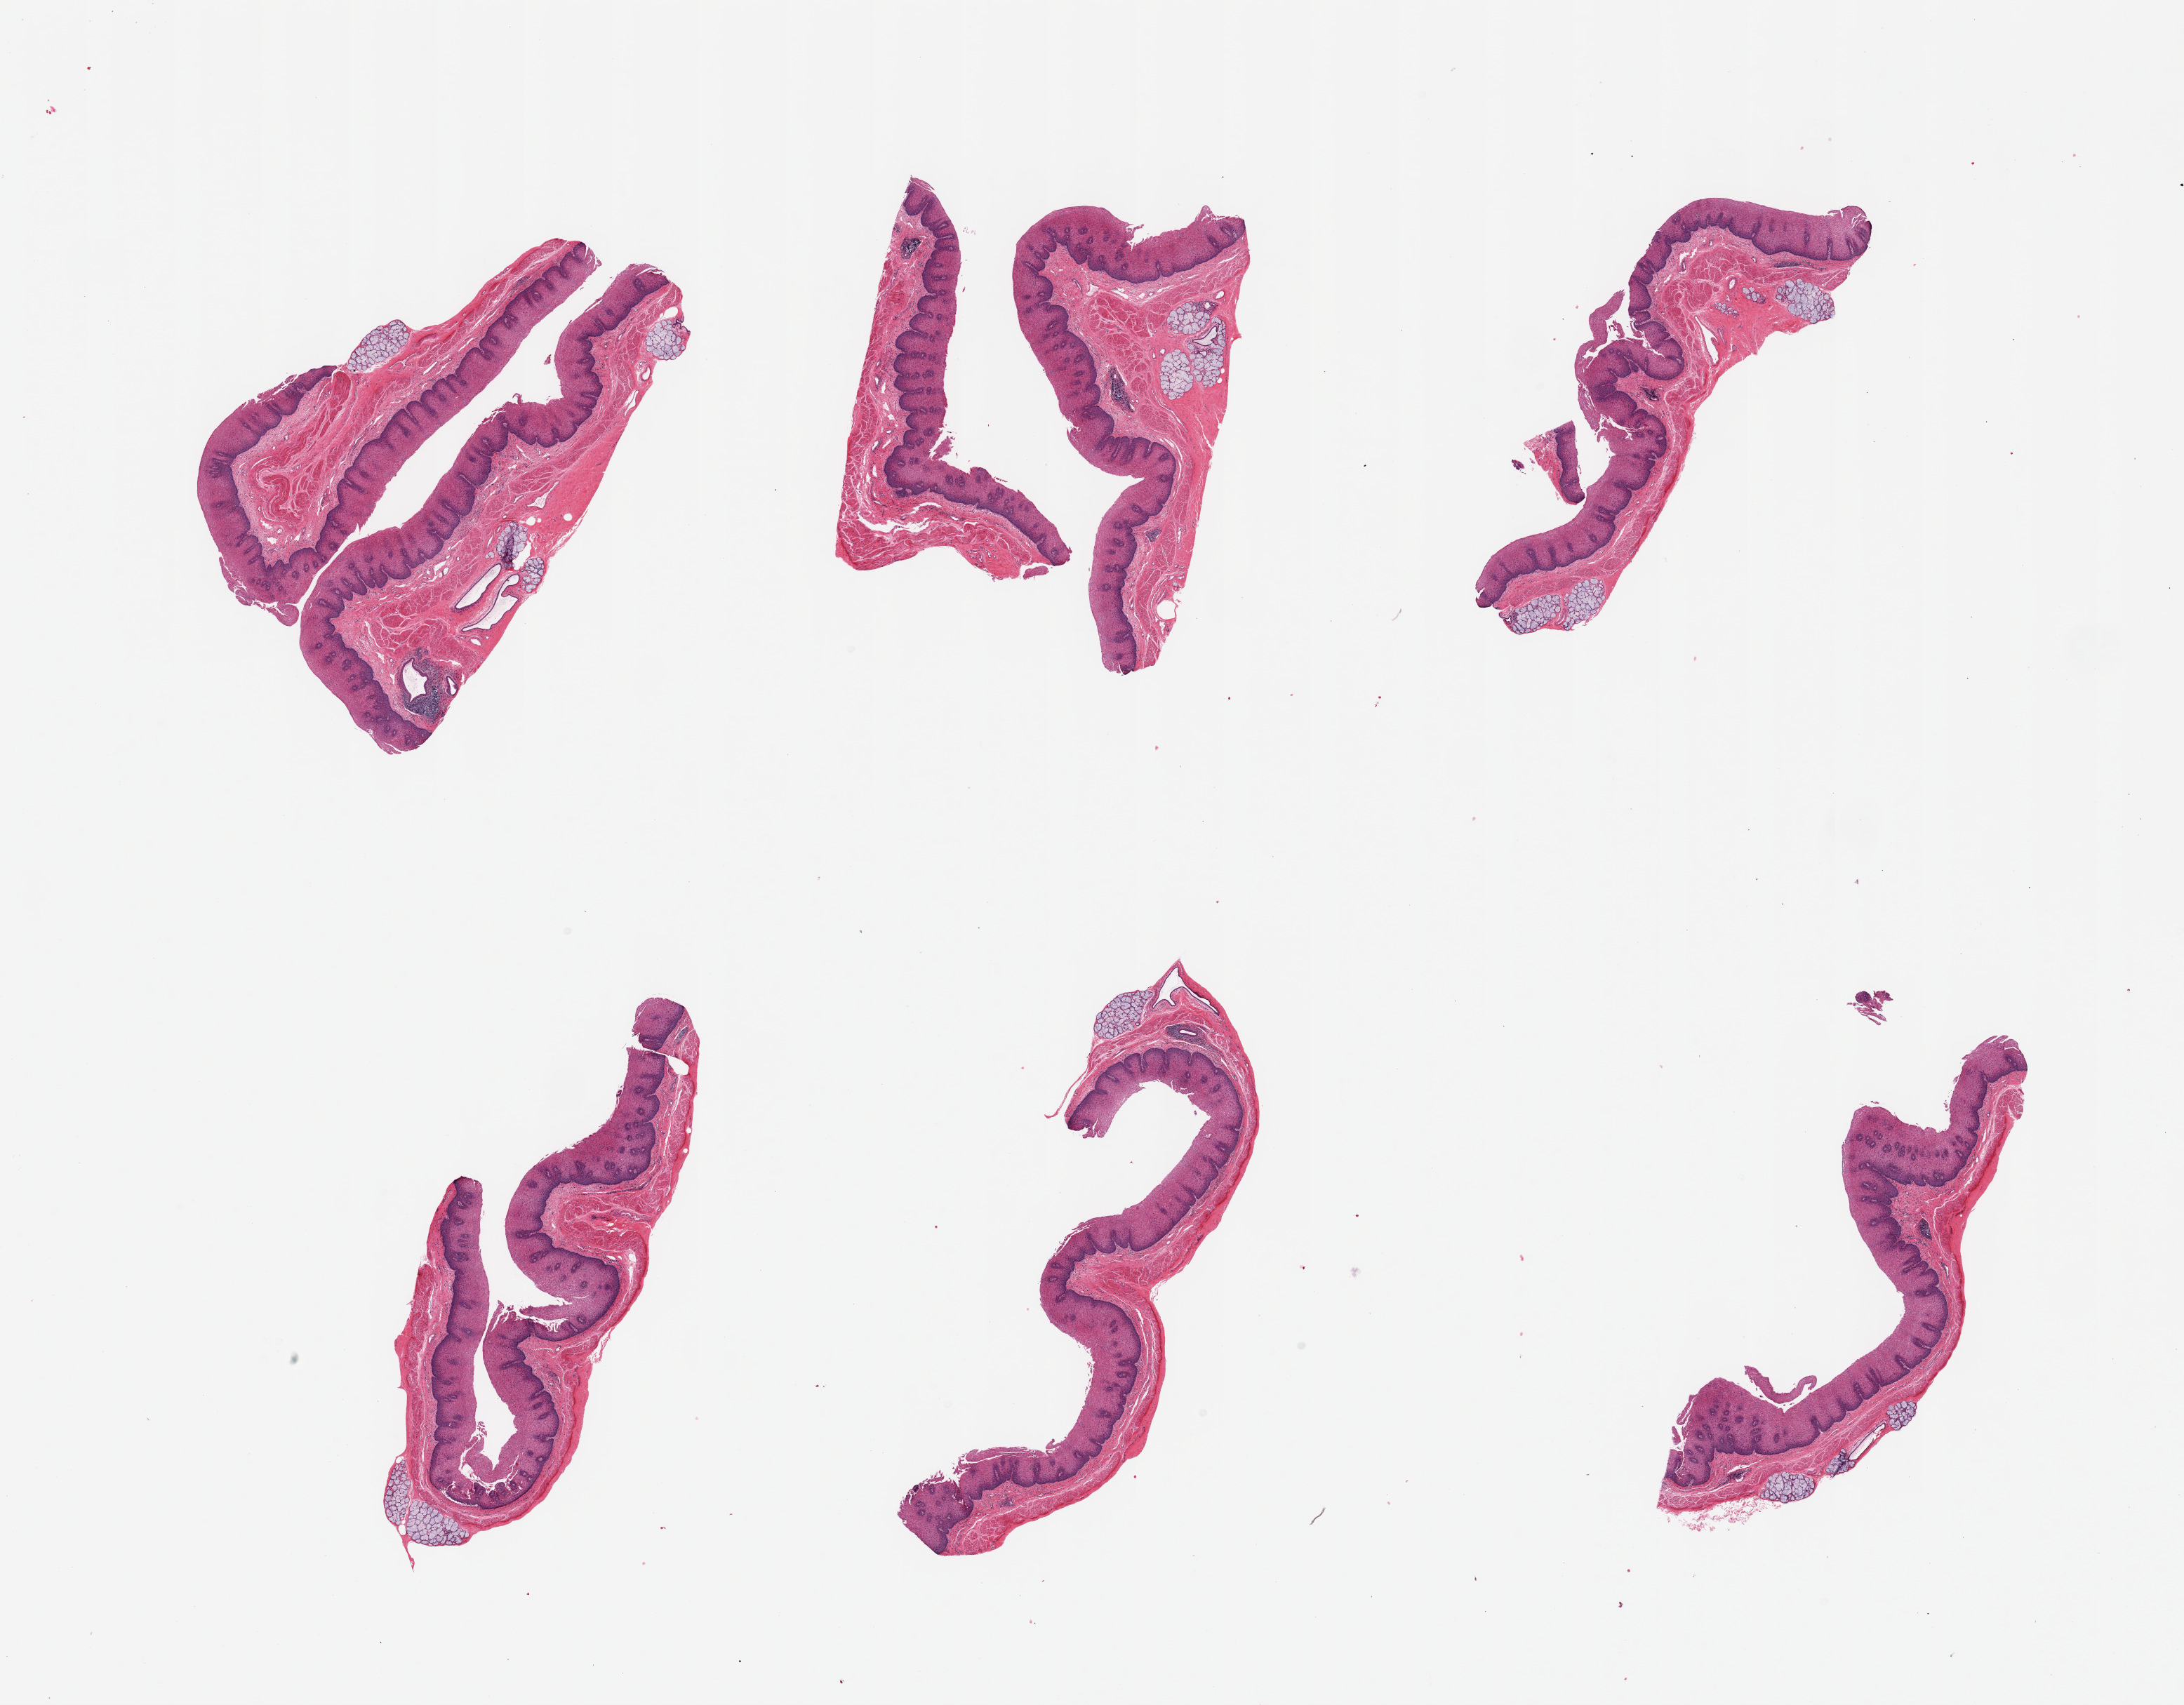
Whole-slide image, hematoxylin and eosin (H&E) stain, whole scanned area (about 24.6 x 19.2 mm) shown as a low-resolution overview, PAXgene-fixed, paraffin-embedded tissue, target tissue: esophageal mucous membrane, tissue donor sample. Donor sex: male.
Review note (as recorded): 6 pieces, squamous mucosa is ~0.5mm, 20-50% thickness, submucosal mucus glands present.